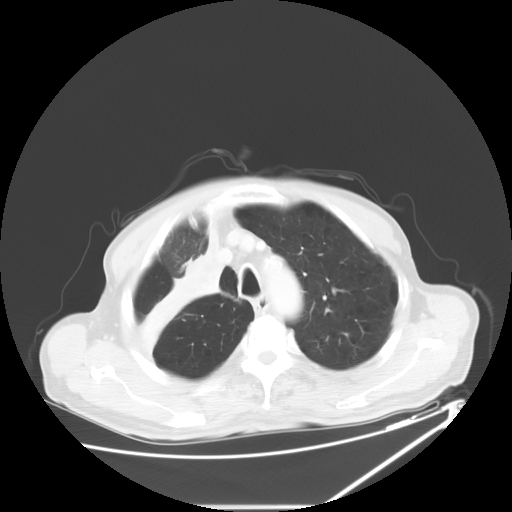
Chest CT, one axial slice; position 49 of 60 along the scan axis; reconstruction kernel STANDARD; lung window (W 1500 / L -600 HU); 5 mm slice thickness; 512 × 512 image matrix, field of view 410 × 410 mm. Patient: male, 73 years. From the clinical record (not read from this slice): clinical TNM (as recorded): T2a N1 M0.
Structures marked on this image (bounding box drawn by a radiologist):
- lung tumour (recorded histology: squamous cell carcinoma): bounding box <142,234,225,349> (left, top, right, bottom; pixels)